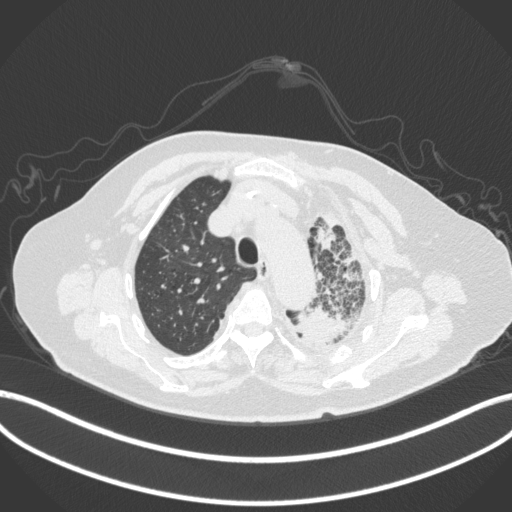
Chest CT, one axial slice; position 308 of 399 along the scan axis; reconstruction kernel B31f; 120 kVp; lung window (W 1500 / L -600 HU); 512 × 512 image matrix, field of view 400 × 400 mm. Patient: female, 75 years. Case-level facts recorded for this patient, not image findings: clinical TNM (as recorded): T3 N3 M1.
Annotated regions visible in this slice (bounding box drawn by a radiologist):
- lung tumour (recorded histology: adenocarcinoma): bounding box (x1, y1, x2, y2) in pixels: (289, 302, 356, 350)